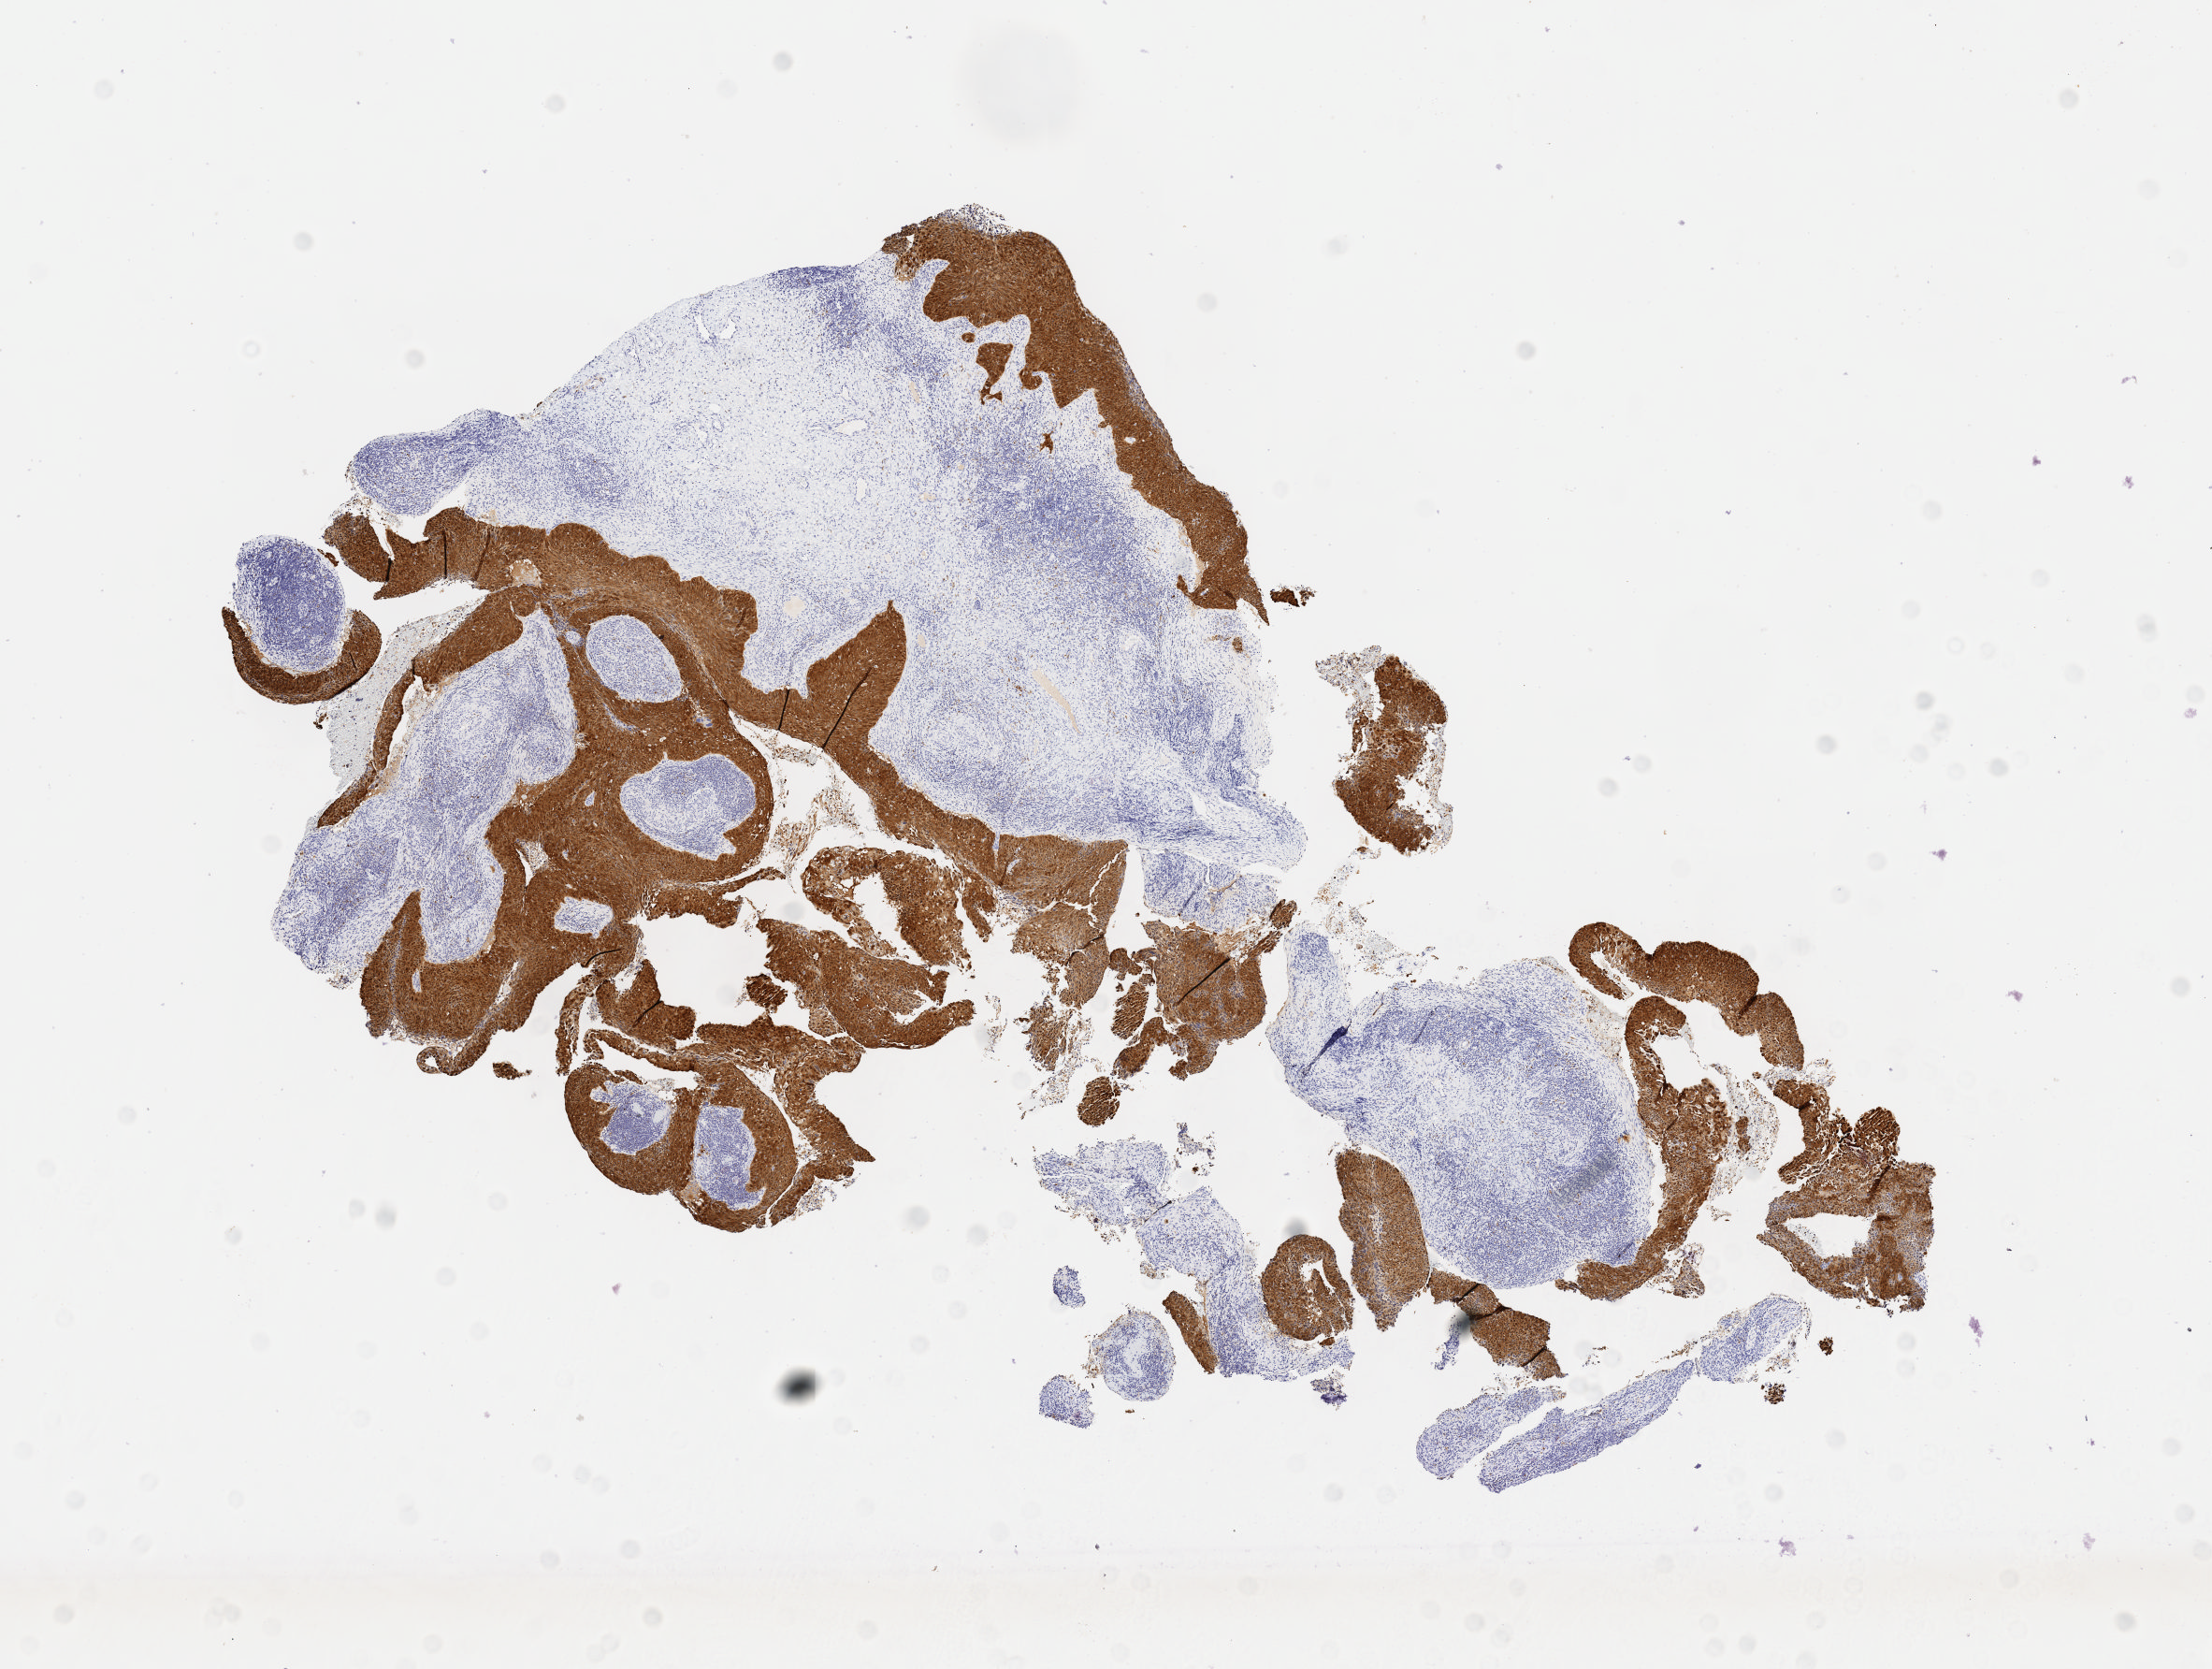
Immunohistochemistry (IHC) whole-slide image stained for p16 (p16INK4a) — low-resolution overview of the scanned area, about 9.6 x 7.2 mm. Specimen: tumor tissue. Site: cervix. Patient female; aged 49.
* diagnosis: Papillary squamous cell carcinoma